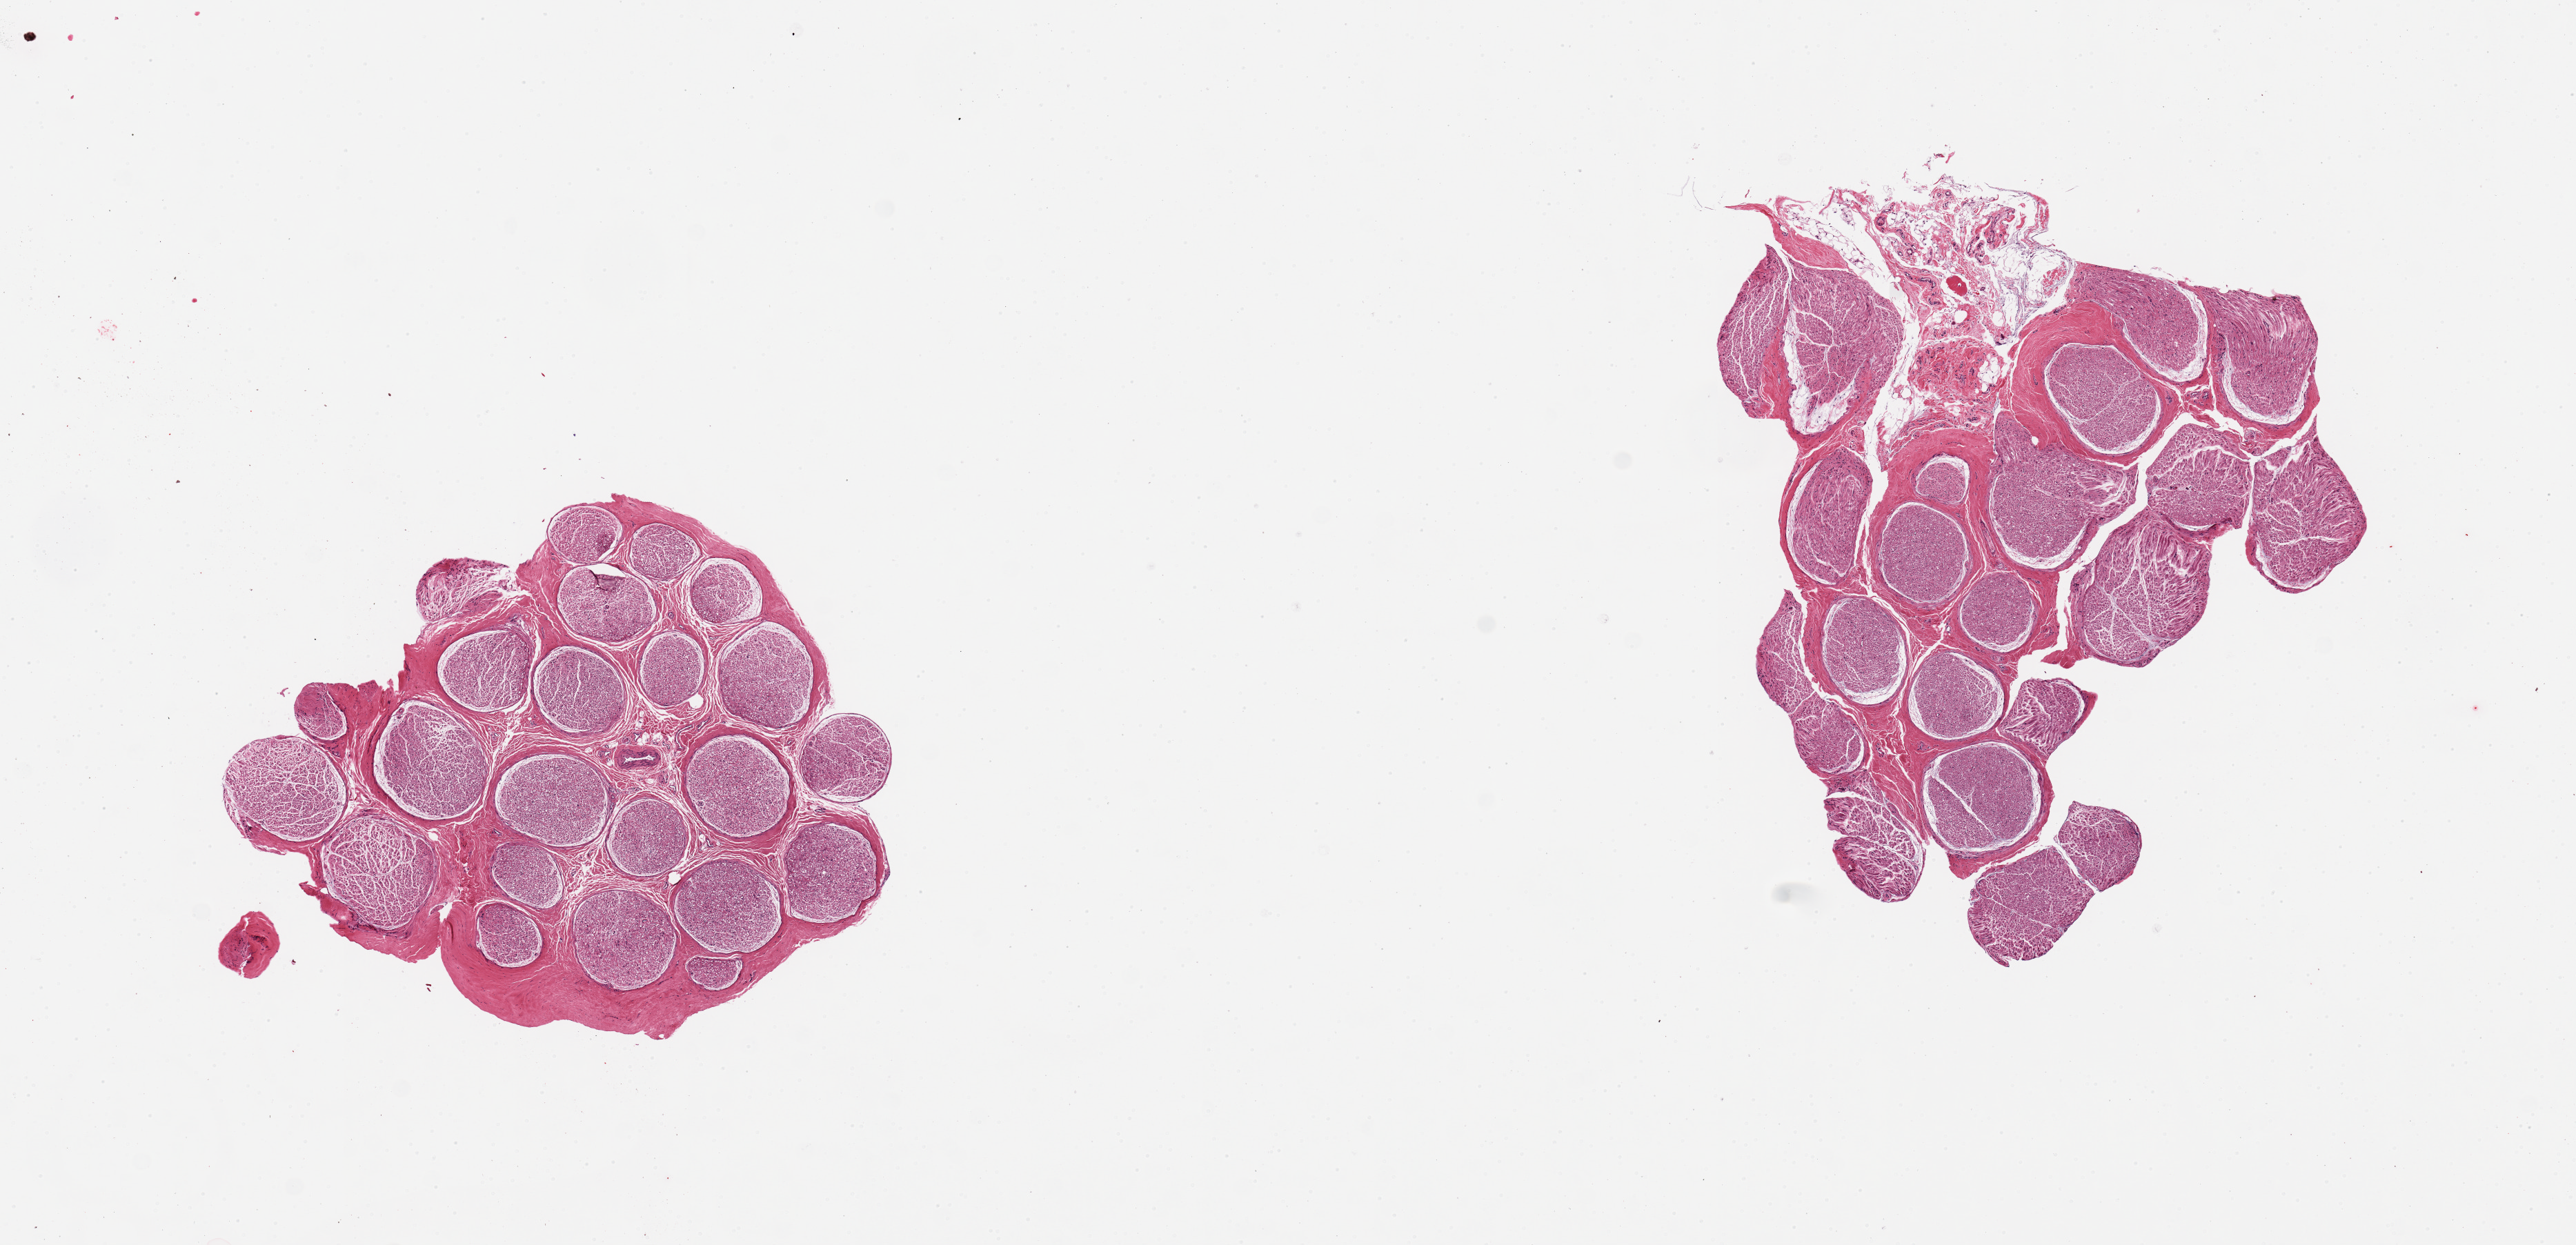
Whole-slide image, hematoxylin and eosin (H&E) stain, brightfield — whole scanned area (about 14.8 x 7.1 mm) shown as a low-resolution overview. PAXgene-fixed, paraffin-embedded tissue. Sampled site (target tissue): tibial nerve. Donor tissue sample. Male donor.
* review note (as recorded): 2 pieces; well trimmed except for internal 20% fatty connective tissue